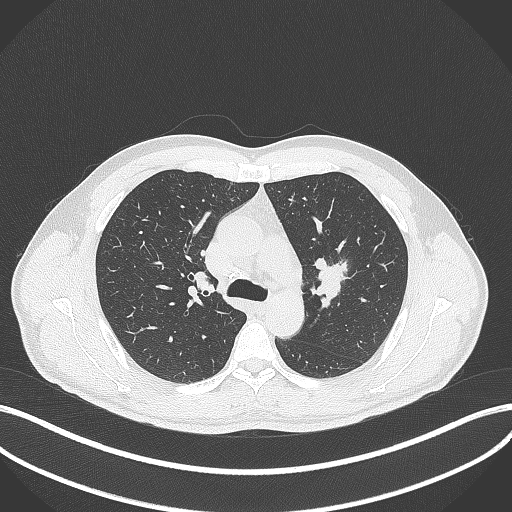
Chest CT, one axial slice. Slice 283 of 392 in the series (ordered by position). Reconstruction kernel B70f. 120 kVp. Lung window (W 1500 / L -600 HU). 1 mm slice thickness. 512 × 512 image matrix, field of view 400 × 400 mm. Male patient, age 50 years. From the clinical record (not read from this slice): clinical TNM (as recorded): T1c N1 M1b.
Annotated regions visible in this slice (bounding box drawn by a radiologist):
- lung tumour (recorded histology: squamous cell carcinoma): bounding box (x1, y1, x2, y2) in pixels: (309, 253, 350, 308)